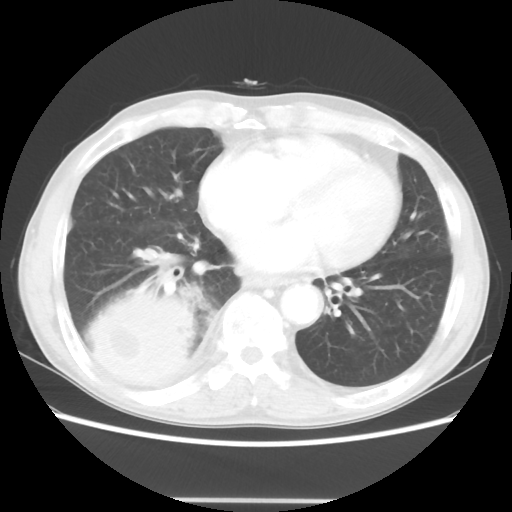
Chest CT, one axial slice. Position 15 of 48 along the scan axis. Lung window (W 1500 / L -600 HU). 5 mm slice thickness. 512 × 512 image matrix, field of view 361 × 361 mm. Patient: male, 66 years. From the clinical record (not read from this slice): clinical TNM (as recorded): T4 N1 M1; histopathological grade: G3.
Annotated regions visible in this slice (rectangle marked by the reading radiologist):
- lung tumour (recorded histology: small cell carcinoma): box from (x=84, y=280) to (x=201, y=396) px